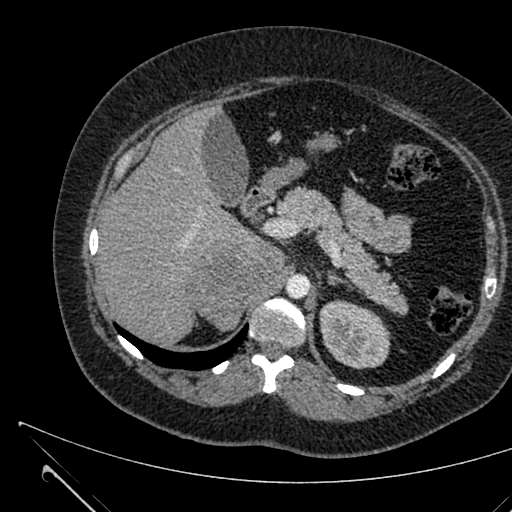
Contrast-enhanced abdominal CT, one axial slice; position 435 of 731 along the scan axis; 120 kVp; soft-tissue window (W 400 / L 40 HU); 1 mm slice thickness; 512 × 512 image matrix, field of view 376 × 376 mm. Patient: female, 36 years. From the clinical record (not read from this slice): diagnosis: adrenocortical carcinoma; tumour side: right adrenal.
Outlined on this slice (semi-automatically segmented with operator editing):
- mass: bounding box (x1, y1, x2, y2) in pixels: (188, 242, 283, 329)